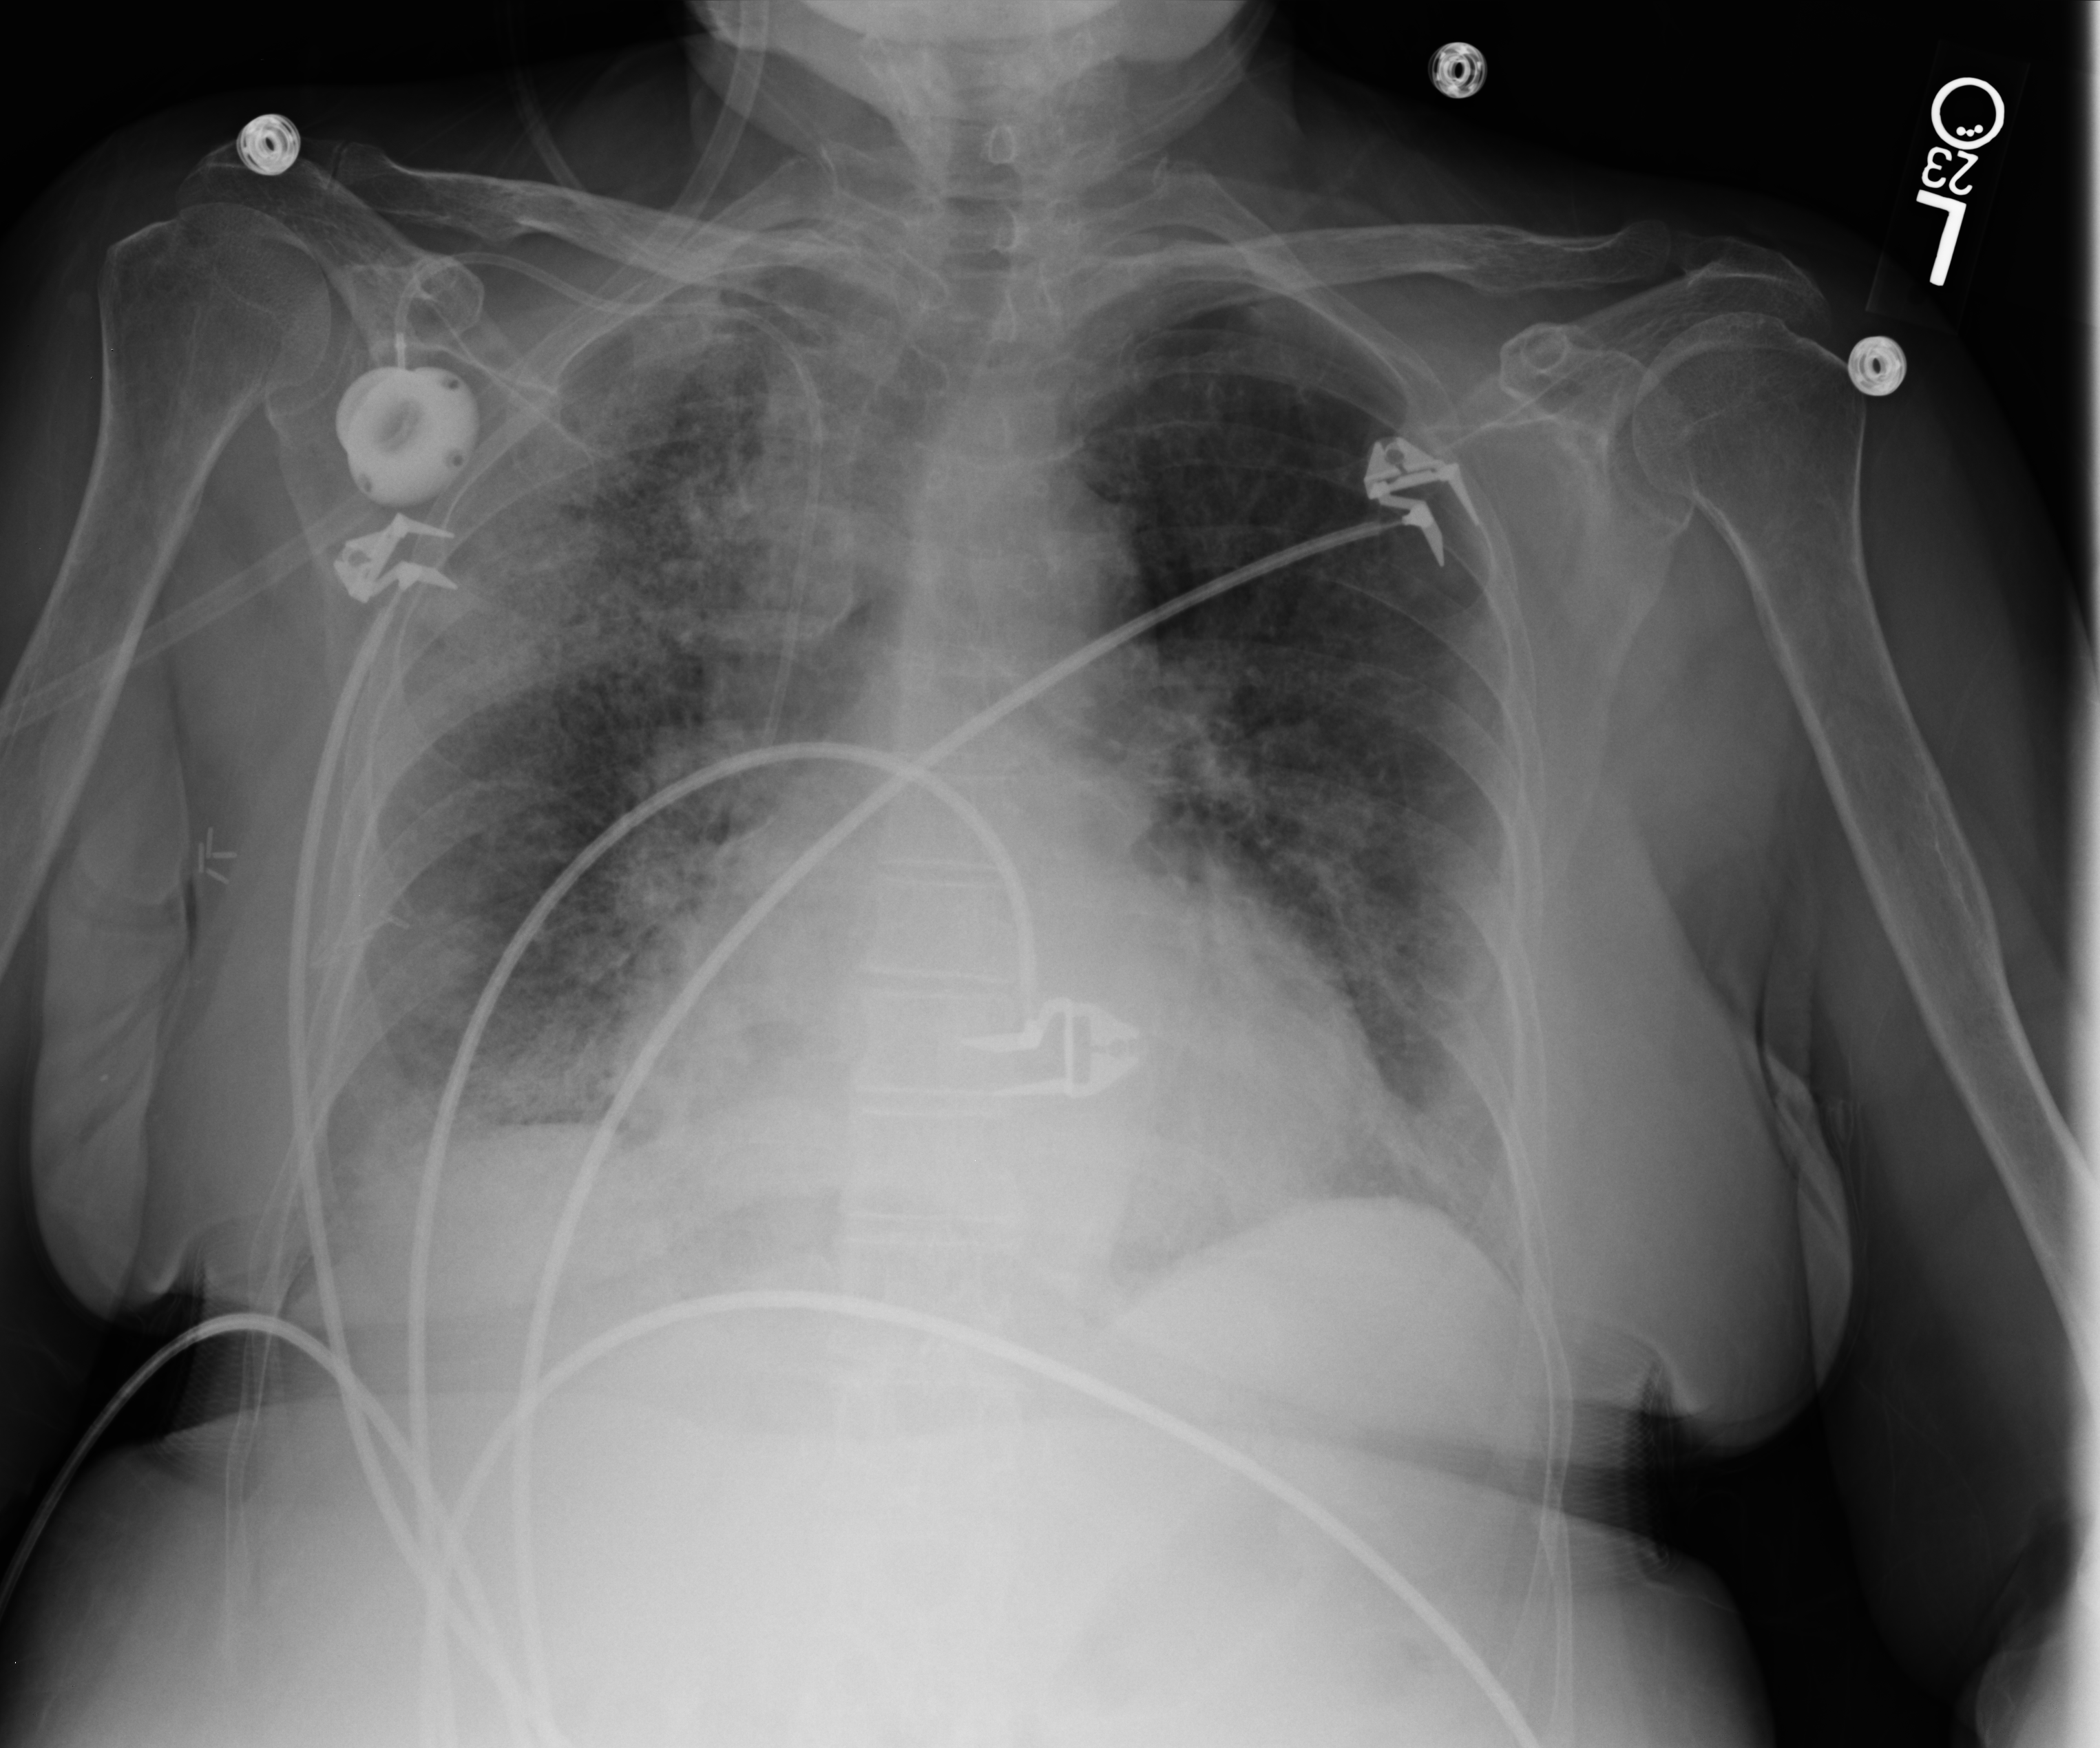
Portable chest radiograph, anteroposterior (AP) projection. Female patient hospitalised with COVID-19, age 60–74 years.
From the hospital-stay record, not from the radiograph (when in the stay this image was taken is not recorded): mechanically ventilated during this hospital stay: yes.